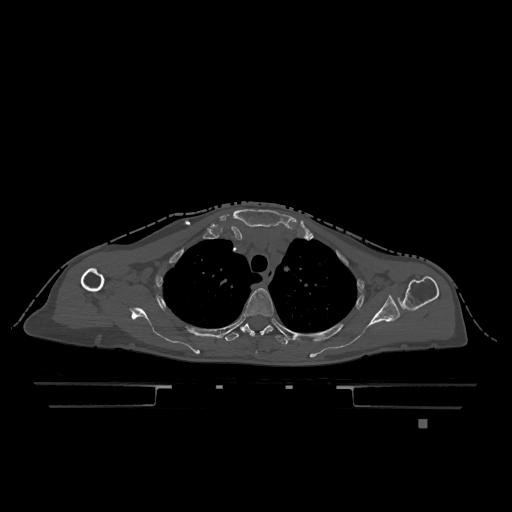
CT including the spine, one axial slice. Slice 906 of 1317 in the series (ordered by position). Bone window (W 1800 / L 400 HU). 0.5 mm slice thickness. 512 × 512 image matrix, field of view 500 × 500 mm. Patient: female, 74 years. Case-level facts recorded for this patient, not image findings: primary cancer: lung; vertebrae with lytic lesions (as recorded): T1, T4, T5, T6, L4, L5.
Outlined on this slice (semi-automatic segmentation, software-assisted and operator-edited):
- T3 vertebra: bounding box [x1, y1, x2, y2] px = [244, 288, 274, 353]
- T4 vertebra: [225, 323, 306, 345]